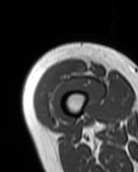
MRI of an extremity soft-tissue mass, one axial slice; slice 11 of 99 in the series (ordered by position); MR volume resampled by the dataset authors to the PET/CT grid (not the native acquisition matrix); 138 × 172 image matrix, field of view 135 × 168 mm. Female patient. Case-level facts recorded for this patient, not image findings: histological type: pleiomorphic undifferentiated sarcoma; grade: high; site of the primary tumour: right quadricep.
Structures marked on this image (expert contour drawn on MRI and transferred to this co-registered scan by the dataset authors):
- gross tumour volume including surrounding oedema: box from (x=37, y=59) to (x=86, y=110) px